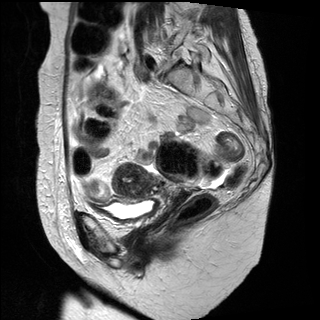
Pelvic MRI for cervical cancer, one sagittal slice; slice 19 of 31 in the series (ordered by position); T2-weighted; 1.5 T; TE 89 ms, TR 3890 ms; 4 mm slice thickness; 320 × 320 image matrix, field of view 260 × 260 mm. Patient: female, 61 years.
Annotated regions visible in this slice (expert manual segmentation):
- uterus and cervix: box from (x=111, y=164) to (x=162, y=199) px